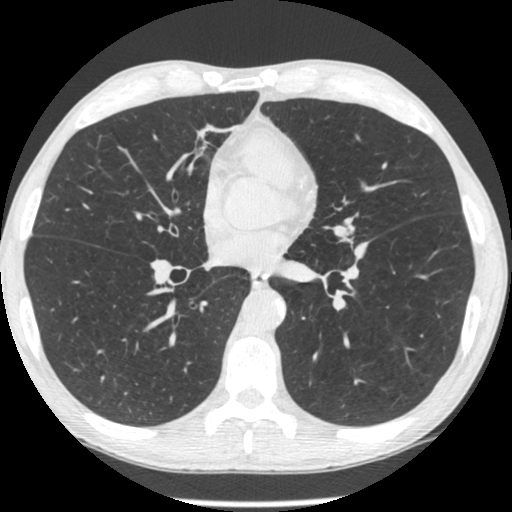
Low-dose screening chest CT, one axial slice. Slice 130 of 293 in the series (ordered by position). Reconstruction kernel STANDARD. Lung window (W 1500 / L -600 HU). 1.25 mm slice thickness. 512 × 512 image matrix, field of view 326 × 326 mm.
Annotated regions visible in this slice (manually delineated by an expert):
- lesion 1 (tumor, upper lobe of left lung): bounding box <354,243,367,258> (left, top, right, bottom; pixels)